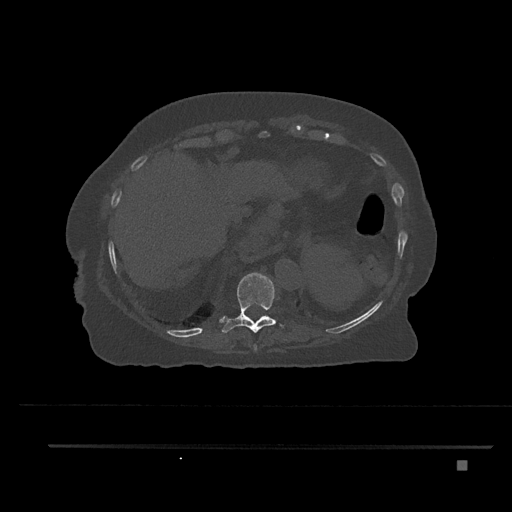
CT including the spine, one axial slice. Slice 354 of 797 in the series (ordered by position). Reconstruction kernel Br40s/3. 120 kVp. Bone window (W 1800 / L 400 HU). 512 × 512 image matrix. Female patient, age 76 years. Case-level facts recorded for this patient, not image findings: primary cancer: lung; vertebrae with lytic lesions (as recorded): T11, L3.
Outlined on this slice (semi-automatically segmented with operator editing):
- T10 vertebra: bounding box (x1, y1, x2, y2) in pixels: (220, 272, 285, 333)
- T9 vertebra: (253, 344, 257, 351)